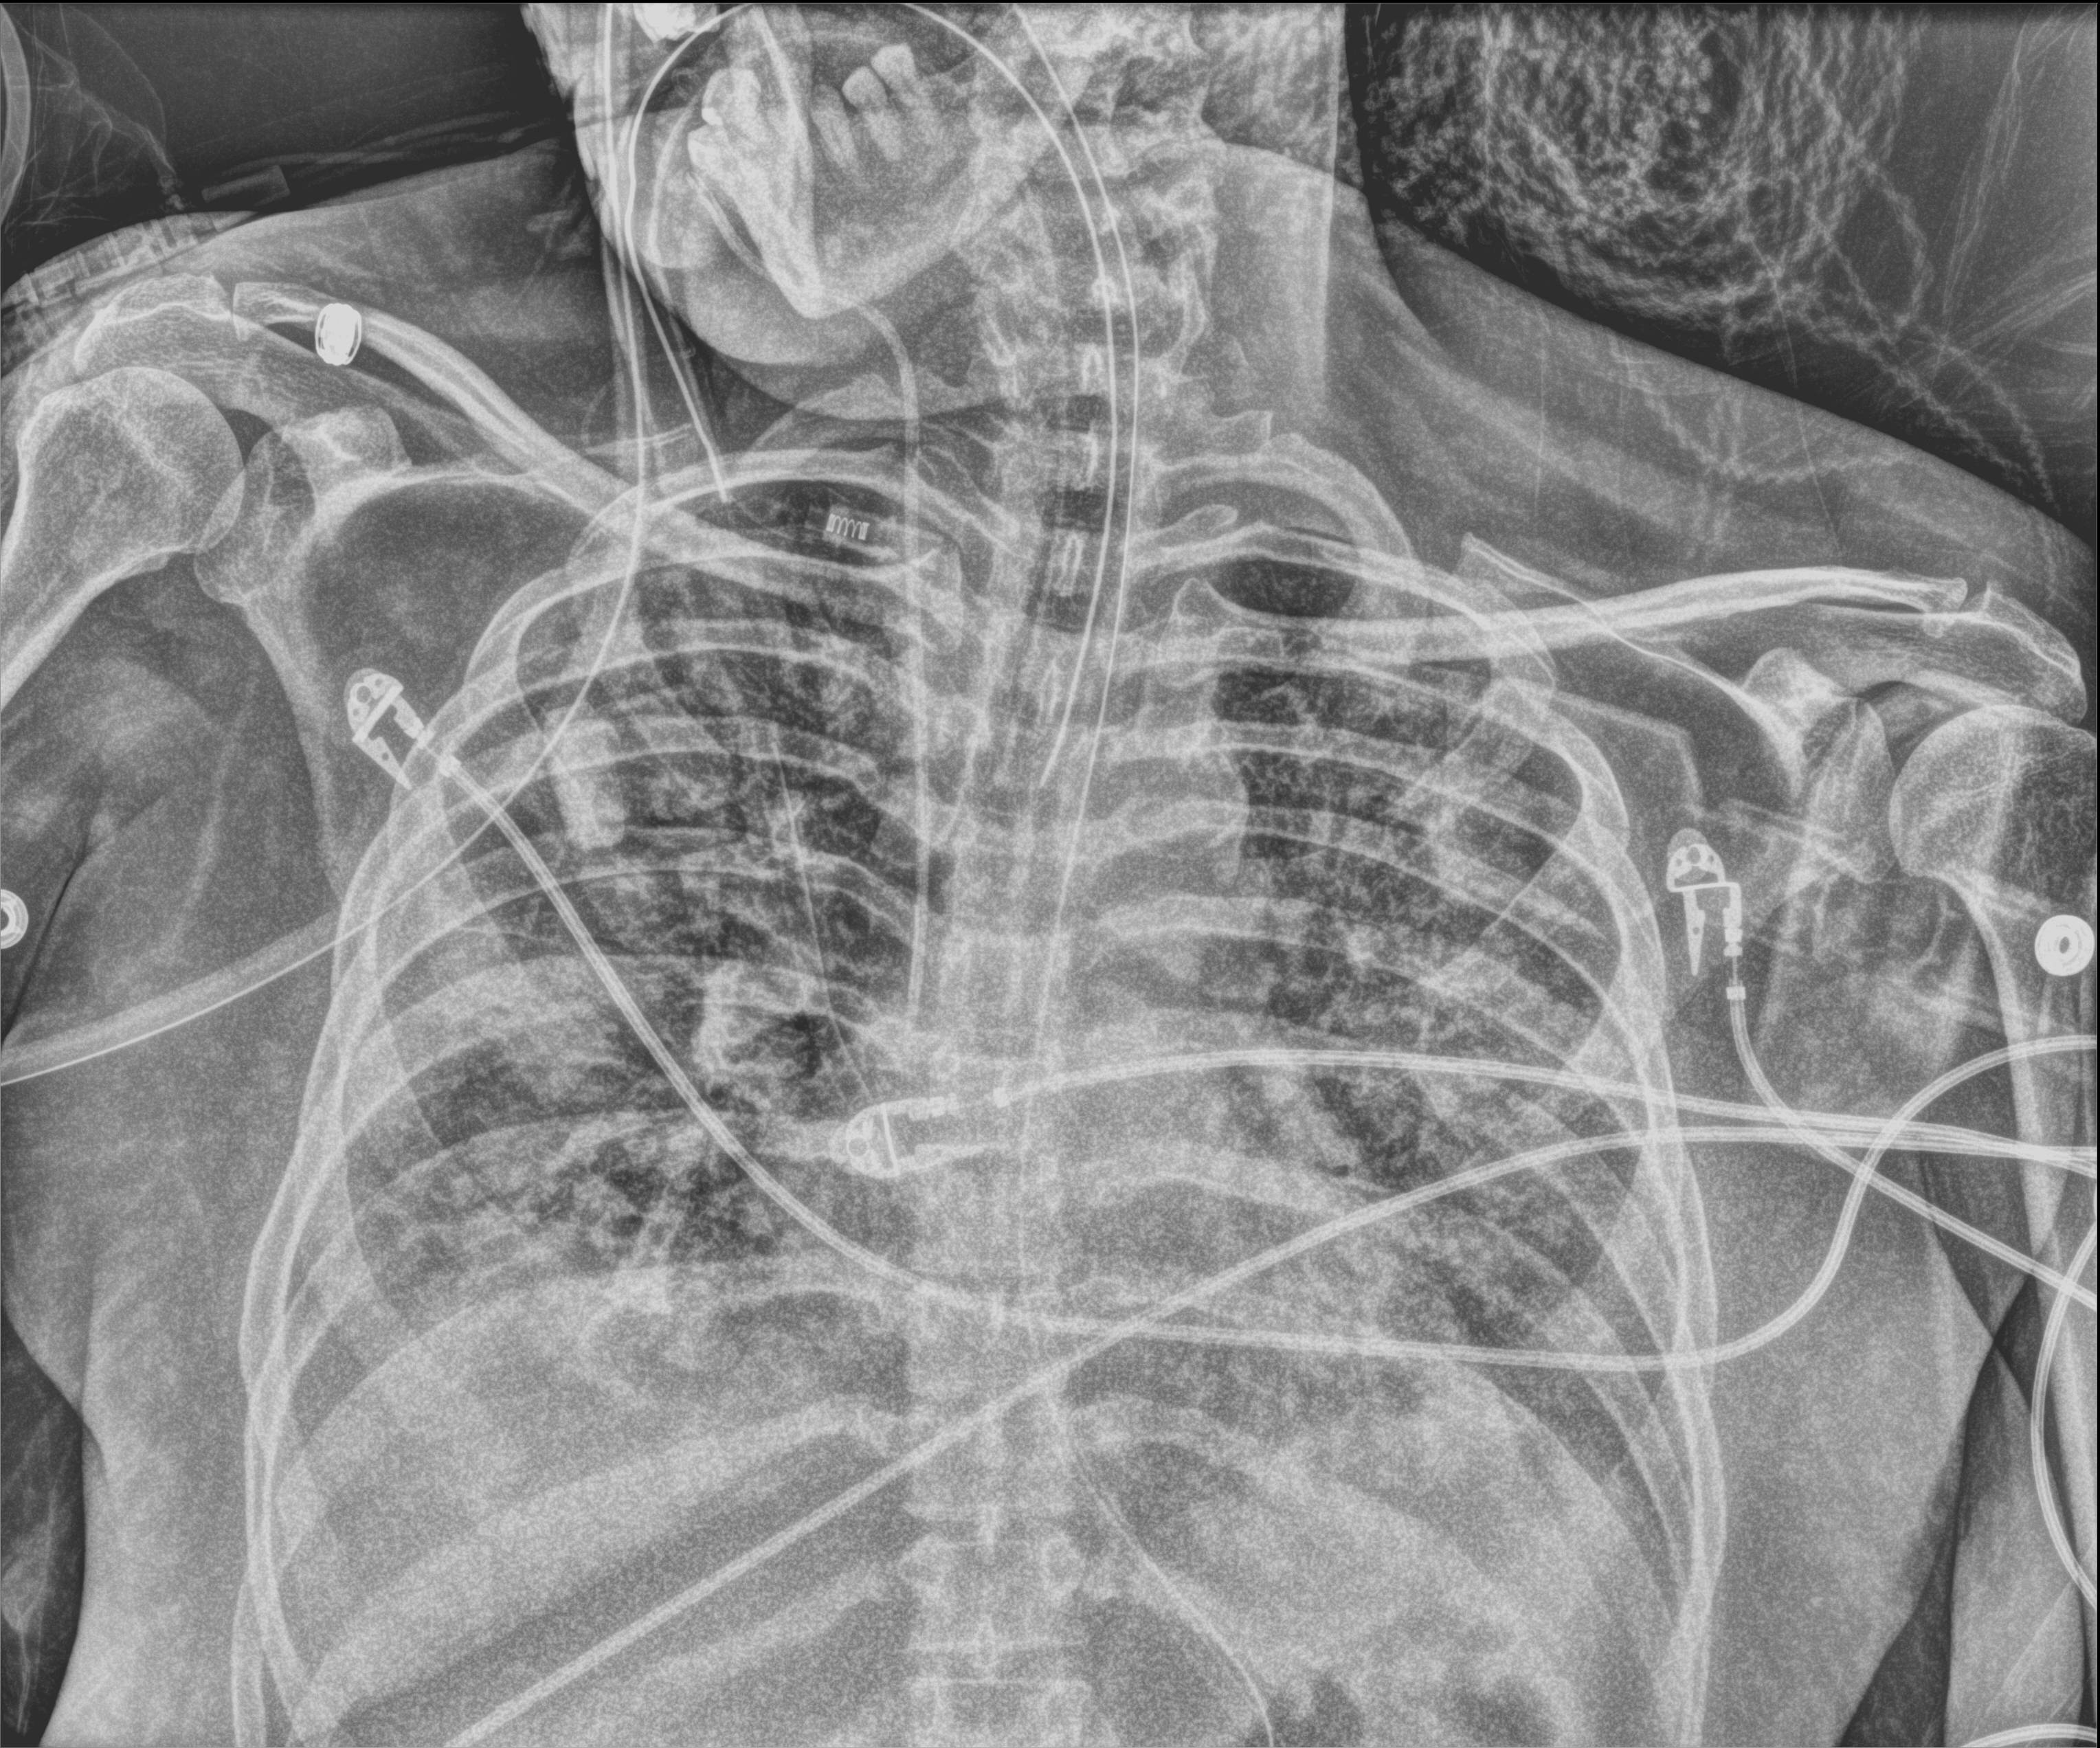
Portable chest radiograph; anteroposterior (AP) projection. Patient hospitalised with COVID-19, aged 18–59 years.
Admission-level facts for this patient (not findings on this image; timing relative to this image not recorded): chronic kidney disease (admission record): no.